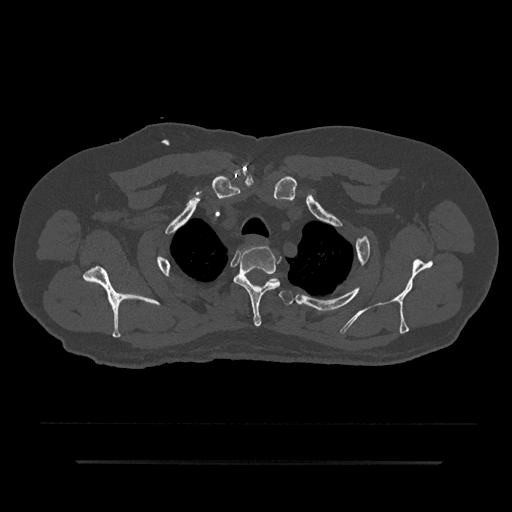
CT including the spine, one axial slice; slice 691 of 797 in the series (ordered by position); reconstruction kernel Br40s/3; 120 kVp; bone window (W 1800 / L 400 HU); 0.5 mm slice thickness; 512 × 512 image matrix, field of view 464 × 464 mm. Patient: male, 59 years. Case-level facts recorded for this patient, not image findings: primary cancer: bile ducts.
Outlined on this slice (semi-automatically segmented with operator editing):
- T2 vertebra: bounding box (x1, y1, x2, y2) in pixels: (233, 245, 281, 327)
- T3 vertebra: (279, 291, 293, 306)